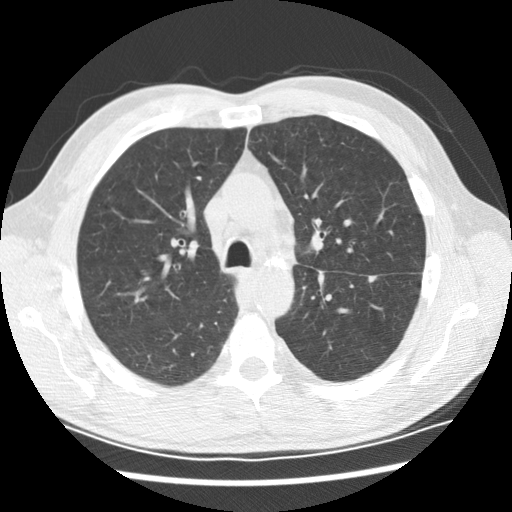
Low-dose screening chest CT, one axial slice. Position 138 of 208 along the scan axis. Reconstruction kernel STANDARD. Lung window (W 1500 / L -600 HU). 2.5 mm slice thickness. 512 × 512 image matrix.
Outlined on this slice (outlined manually by an expert reader):
- lesion 2 (tumor, lower lobe of left lung): bounding box [x1, y1, x2, y2] px = [367, 275, 377, 282]